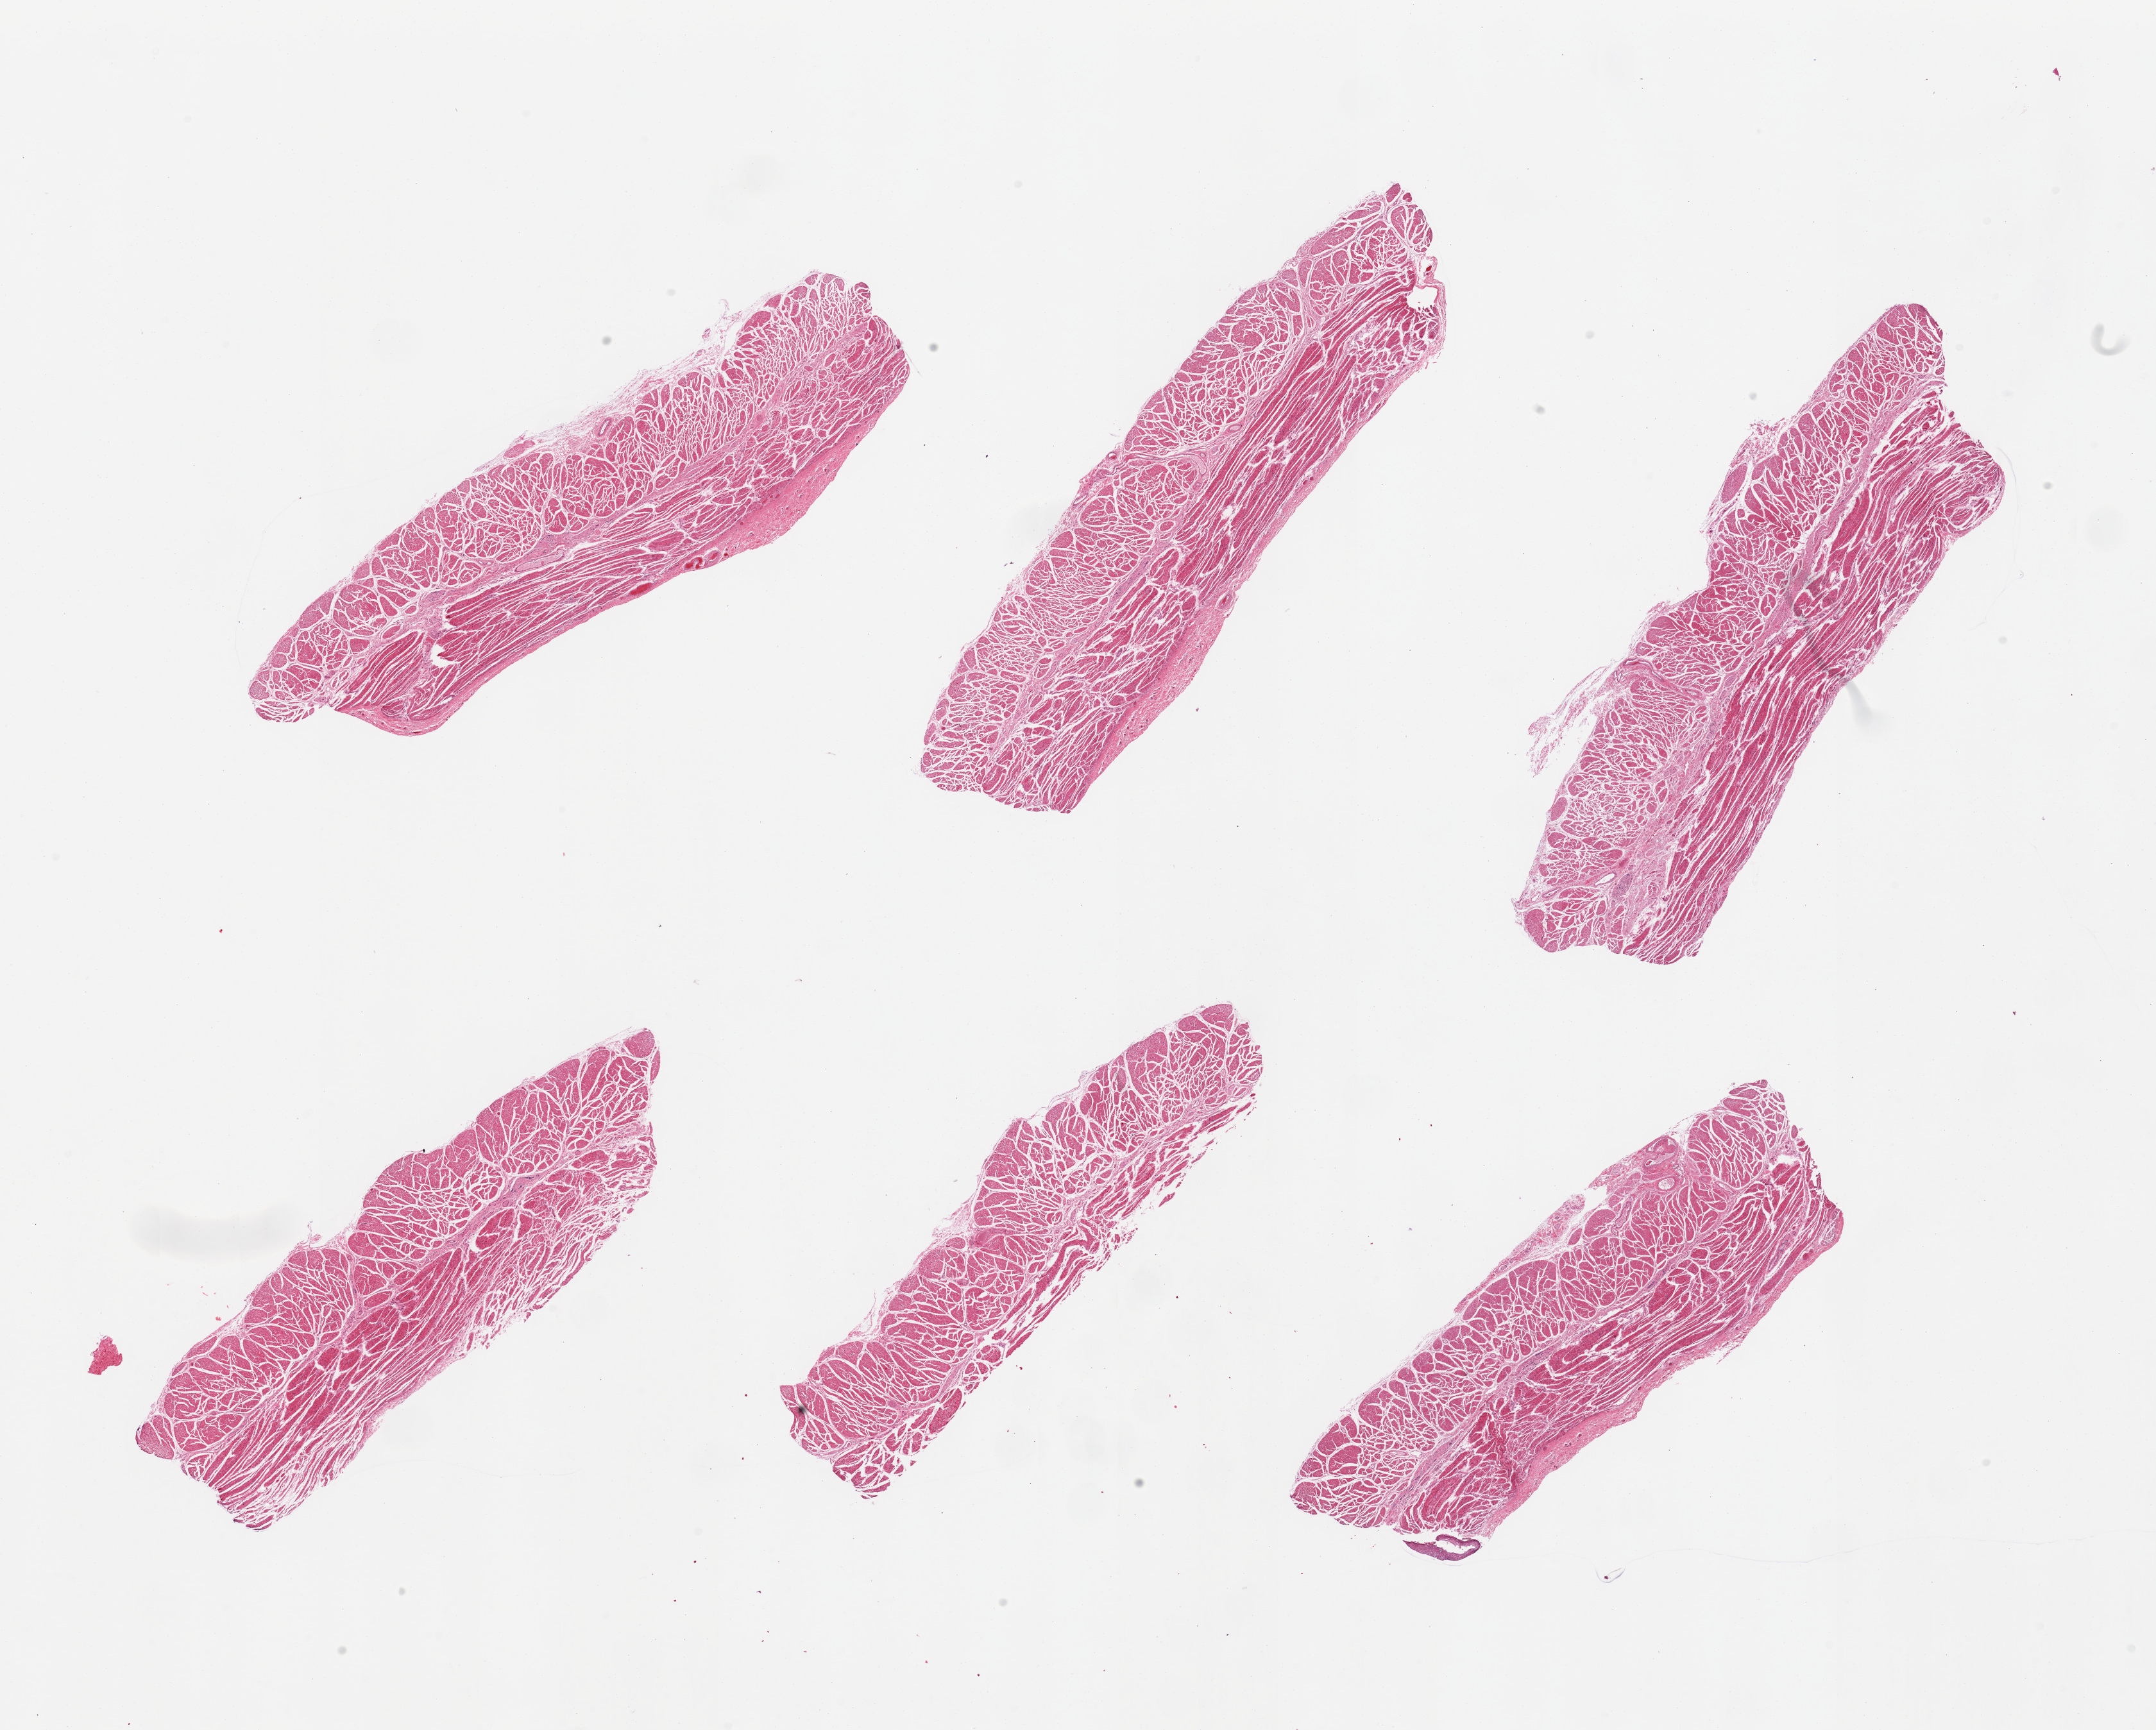
Digitized H&E-stained section, shown as a low-resolution overview of the whole scanned area (about 26.6 x 21.3 mm). PAXgene-fixed, paraffin-embedded tissue. Sampled site (target tissue): esophageal muscle. Donor tissue sample. Donor: male.
* reviewer comment on this tissue sample: 6 pieces; well trimmed target muscularis